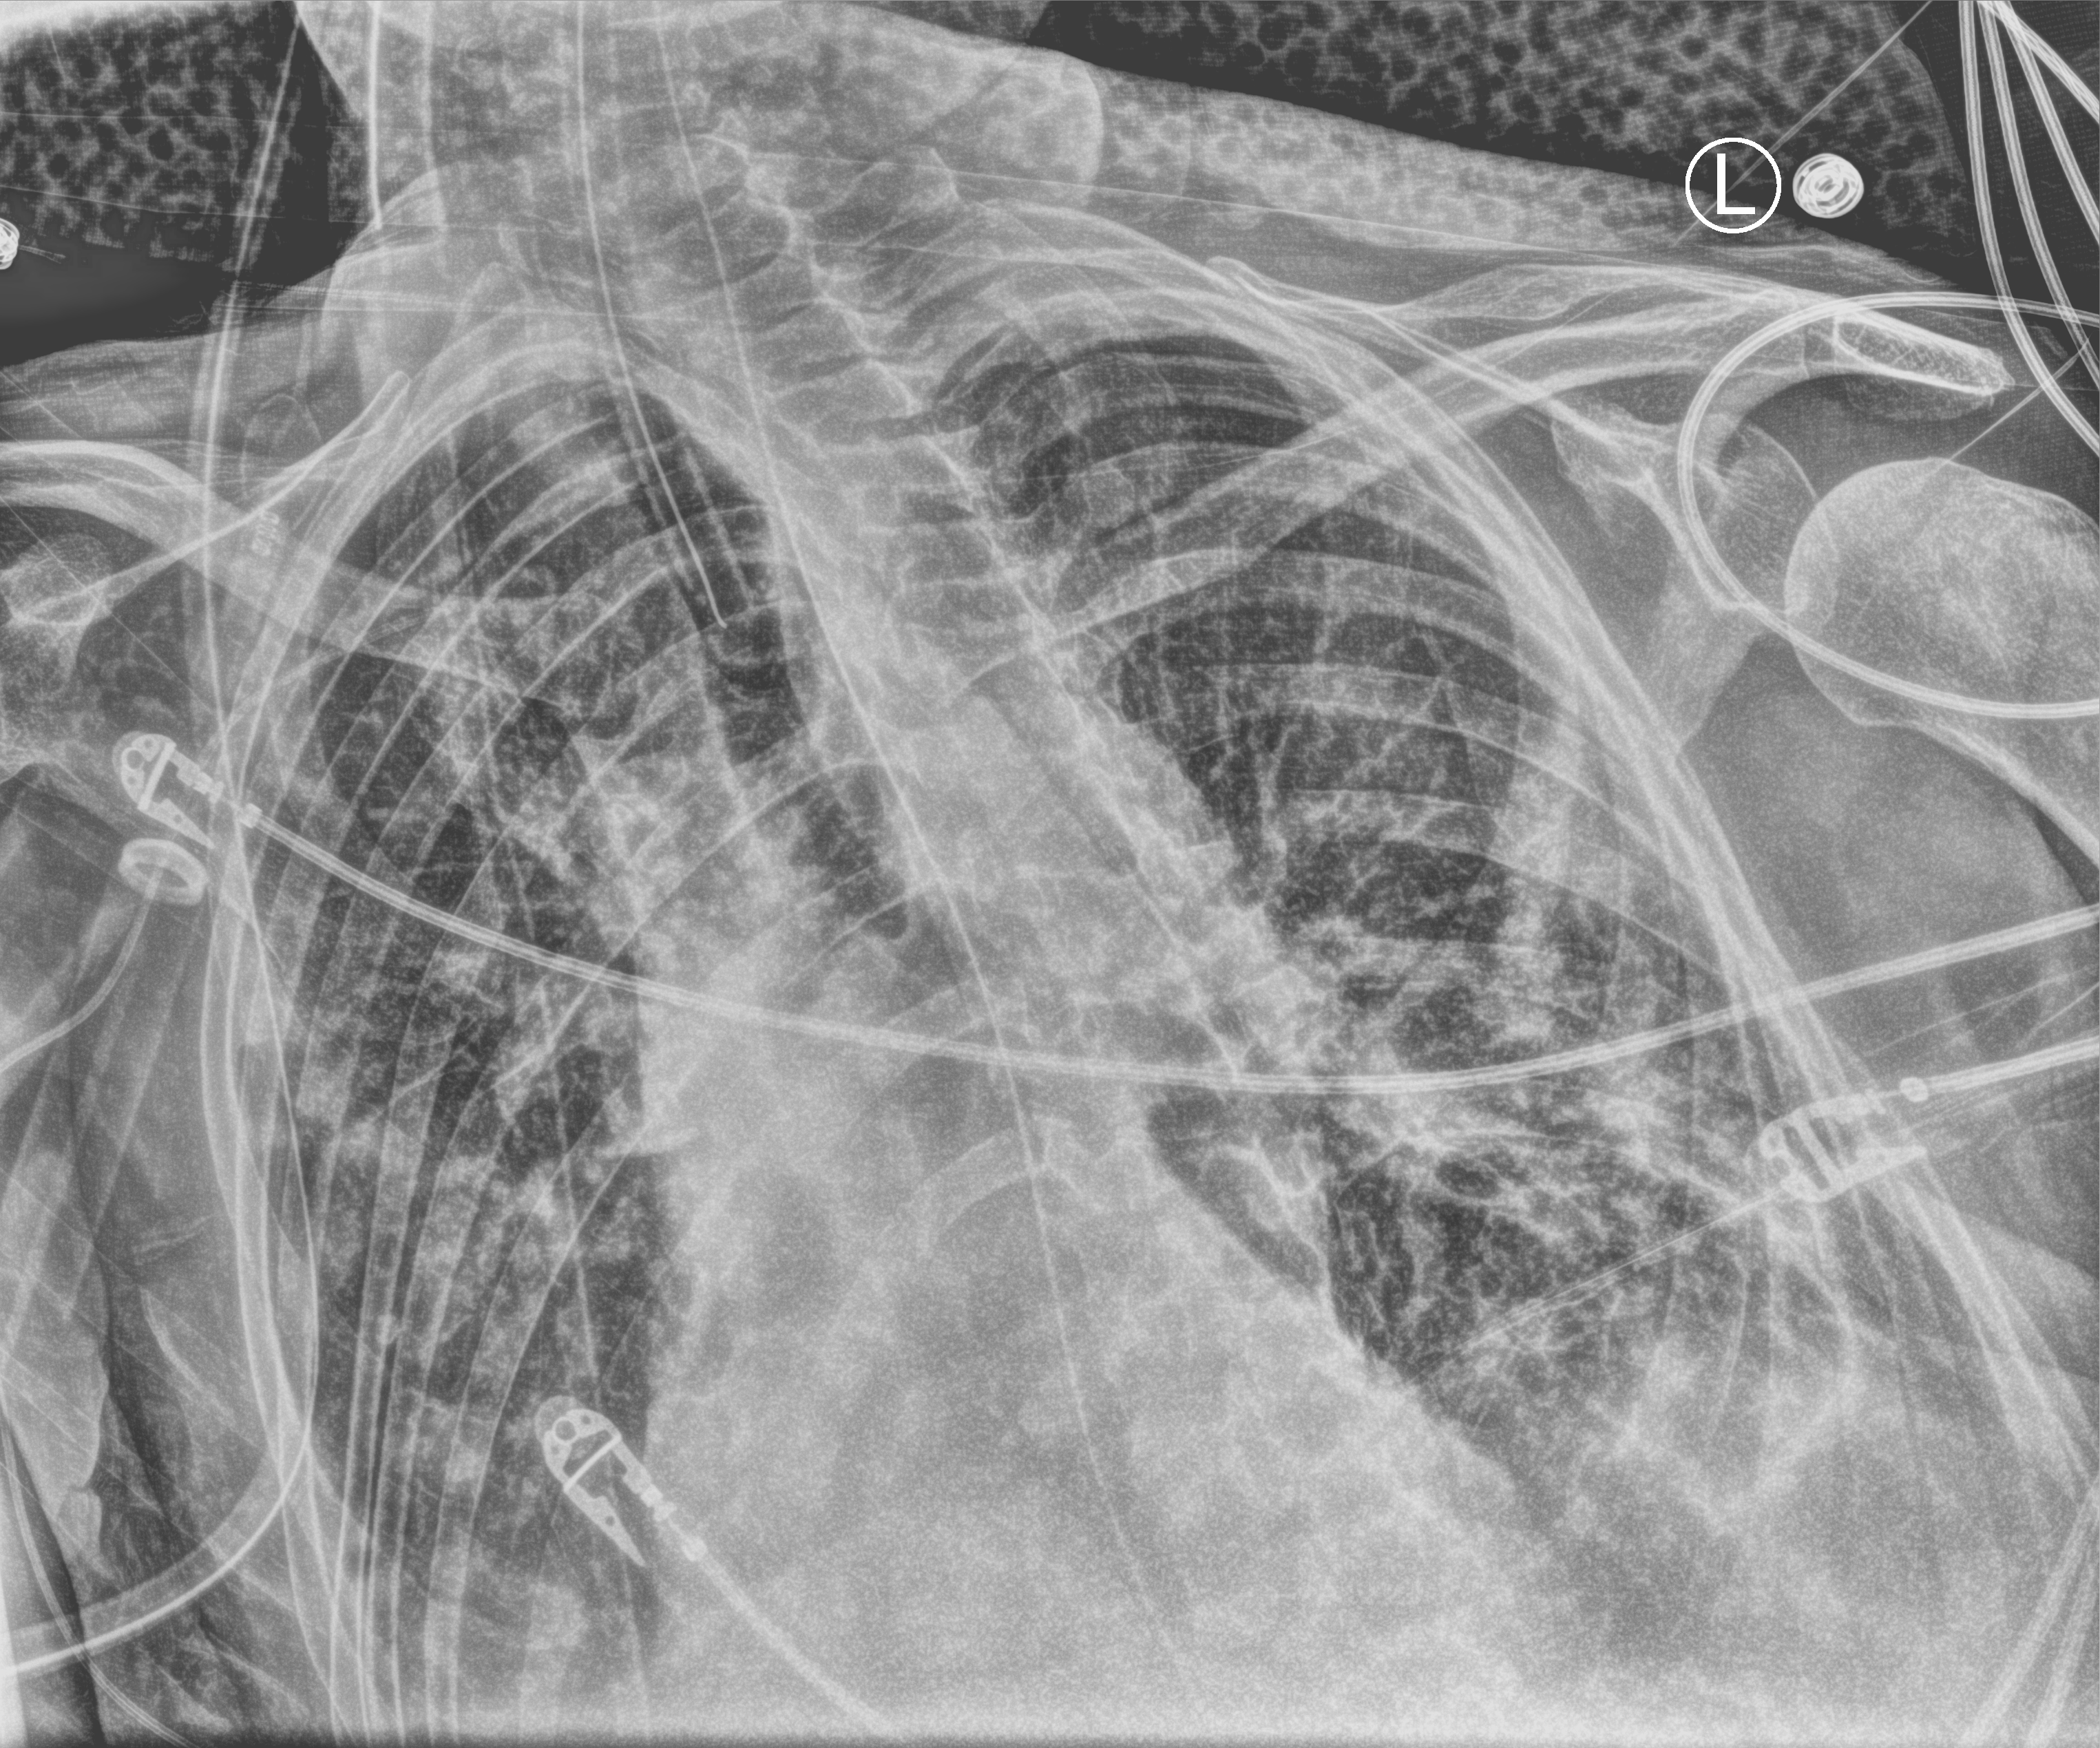
Portable chest radiograph; anteroposterior (AP) projection. Male patient hospitalised with COVID-19, age 75–90 years.
From the hospital-stay record, not from the radiograph (when in the stay this image was taken is not recorded):
- diabetes (admission record): no
- admitted to intensive care during this hospital stay: yes
- smoking status (admission record): never